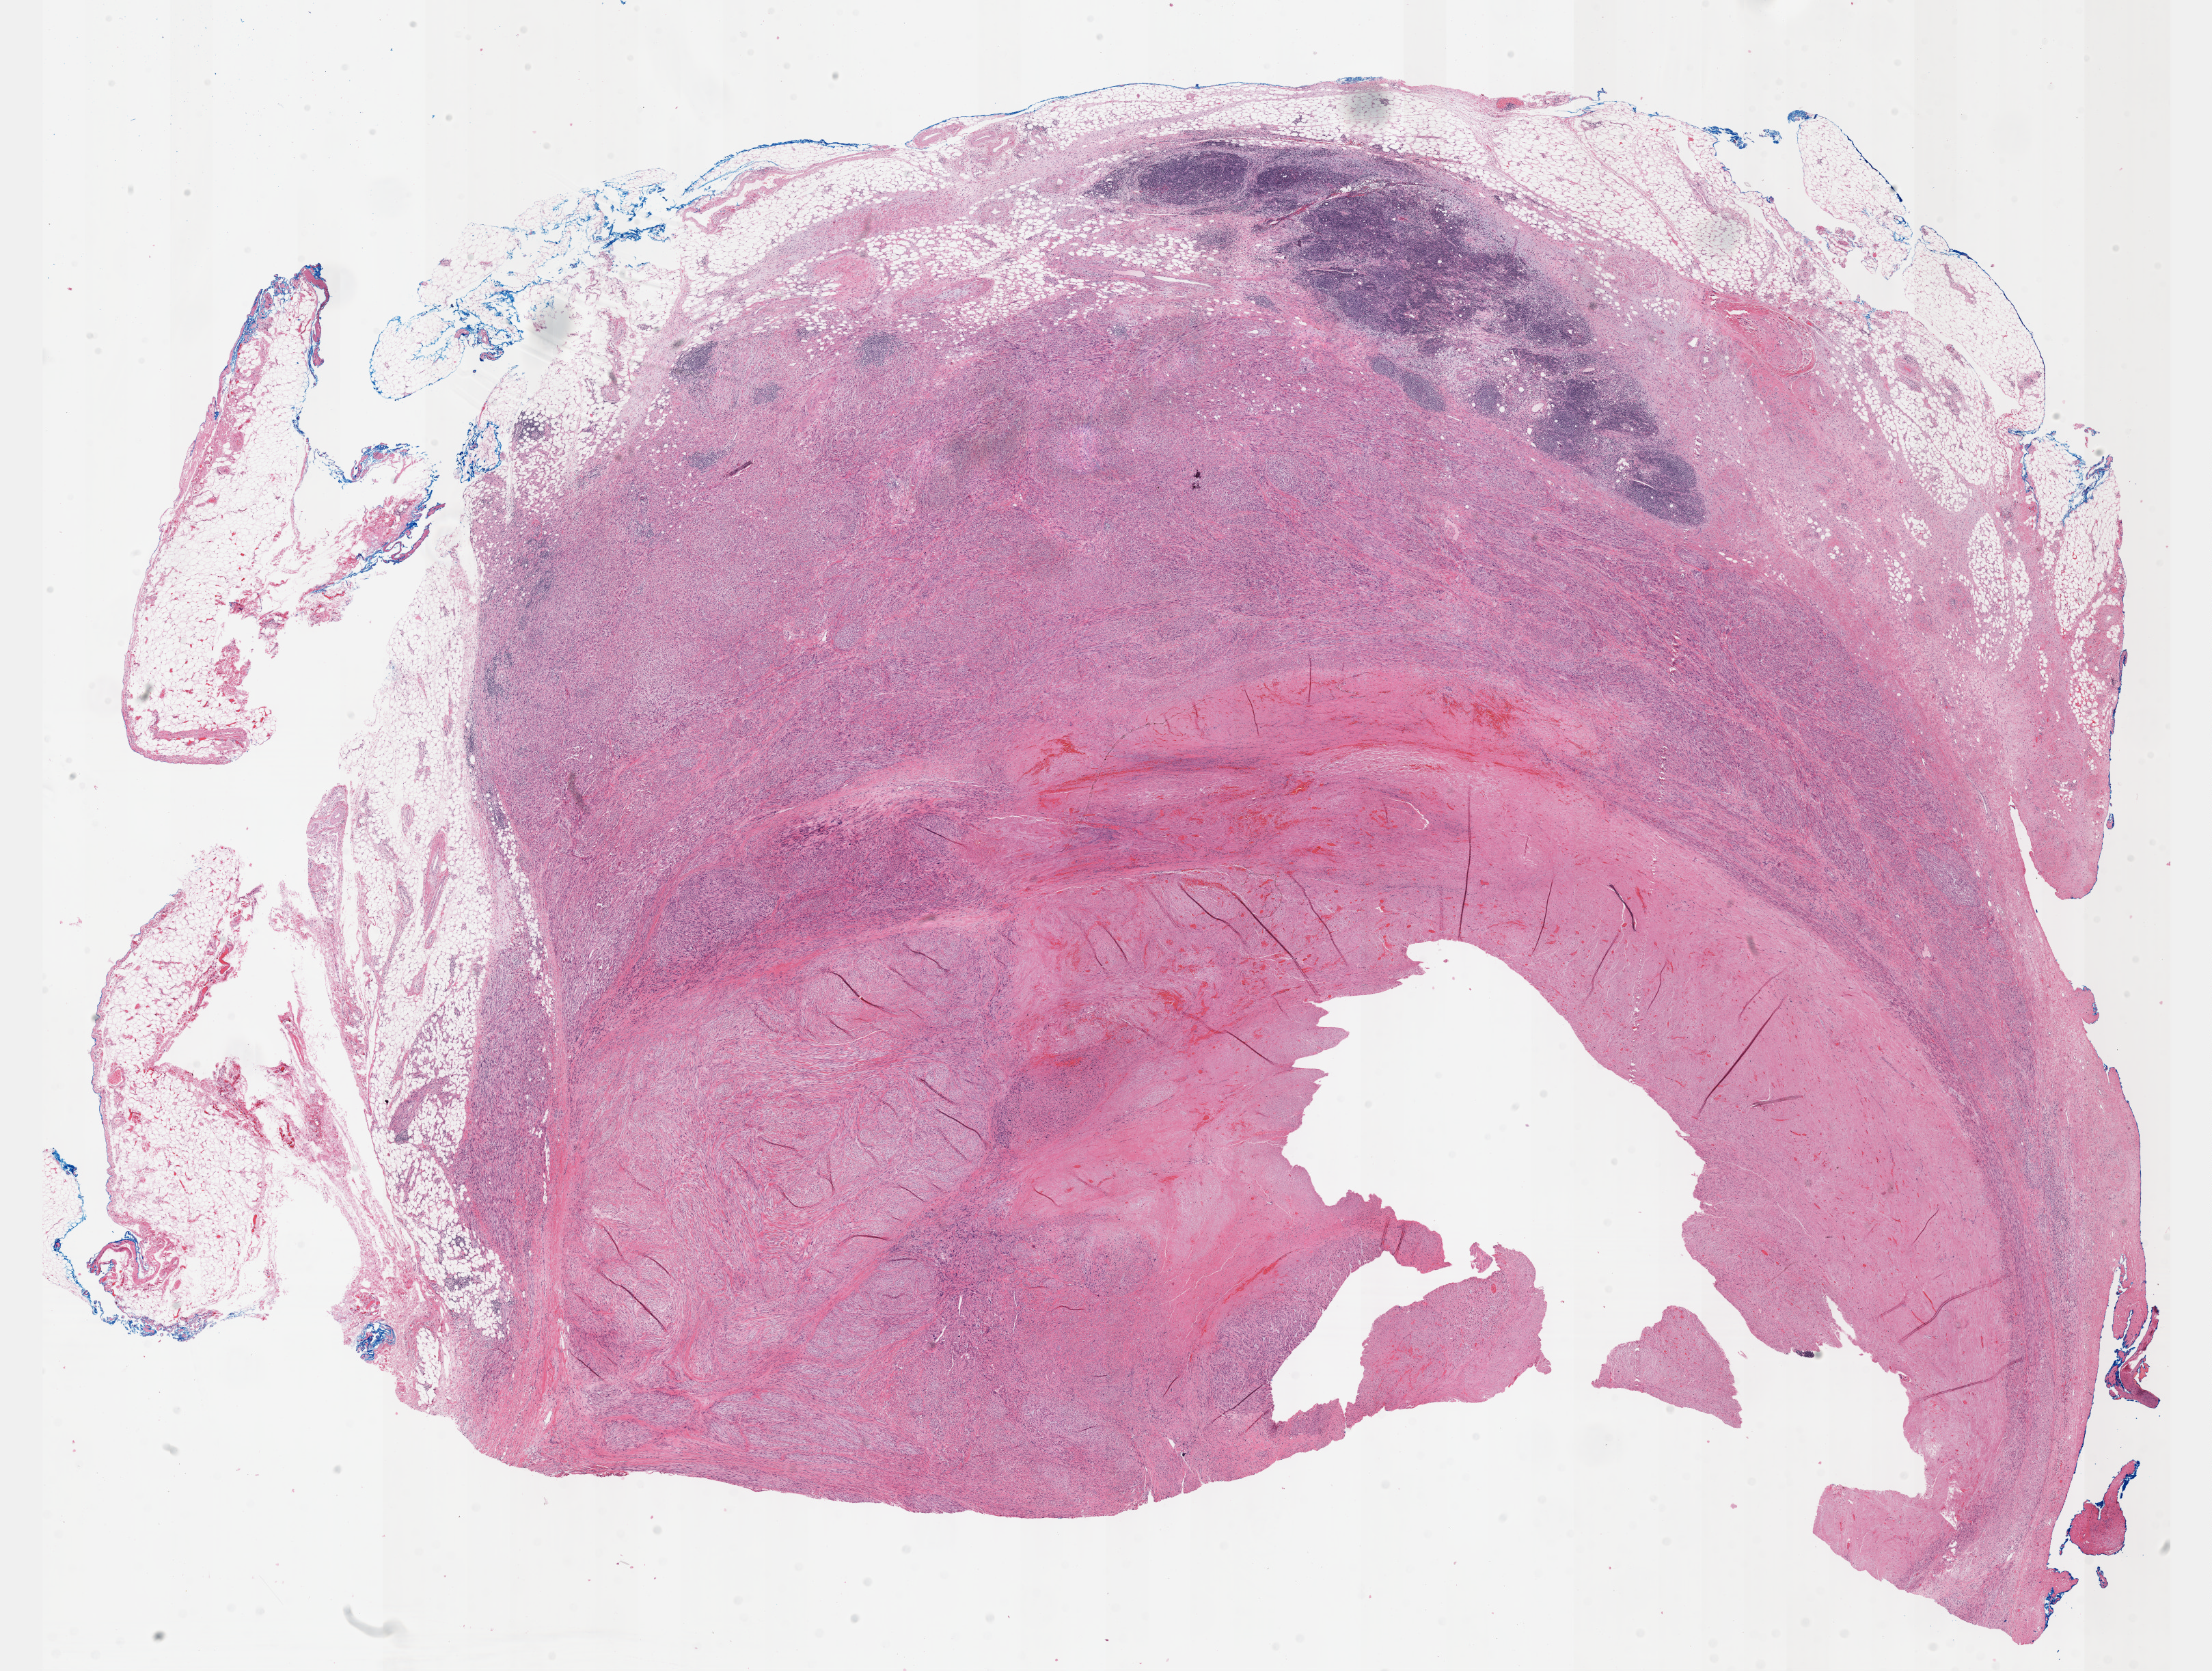
Digitized H&E-stained tissue section (whole slide), whole scanned area (about 26.2 x 19.8 mm) shown as a low-resolution overview, formalin-fixed paraffin-embedded (FFPE) diagnostic section, primary tumour sample from the connective, subcutaneous and other soft tissues. Female patient.
Pathologic diagnosis: Leiomyosarcoma, NOS (connective, subcutaneous and other soft tissues of thorax).